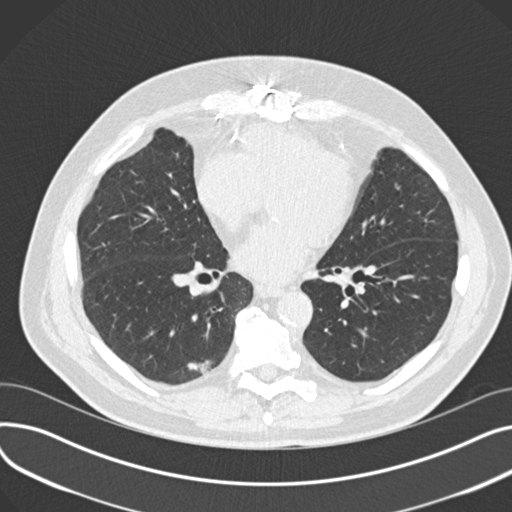
Chest CT (low-dose screening protocol), one axial image, third annual screen, lung window (W 1500 / L -600 HU), 120 kVp, slice 99 of 177 in the series. Male participant, aged 68 years at enrolment. Former smoker at enrolment.
- Expert reader's lesion annotation, bounding box [x1, y1, x2, y2] px = [178, 348, 223, 389].
- The screening reader recorded 4 non-calcified nodules or masses ≥4 mm on this exam (left upper lobe, lingula, right upper lobe, right lower lobe); which of them this box marks is not recorded.
- Official screen result: positive, other.
- Participant outcome: lung cancer diagnosed 68 days after this screen — adenosquamous carcinoma, right lower lobe, moderately differentiated (G2), stage IB (AJCC 6th edition), 31 mm at pathology.